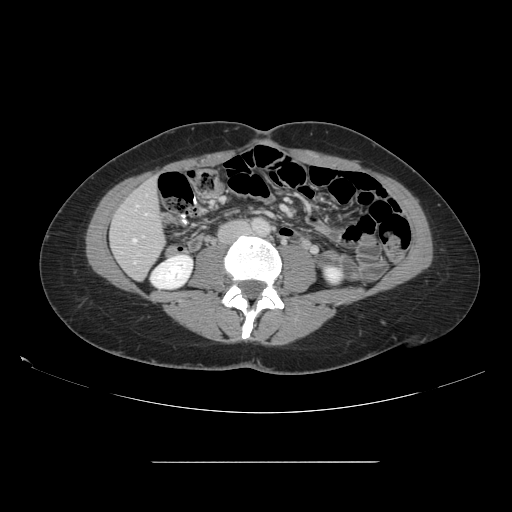
Contrast-enhanced abdominal CT, one axial slice; position 33 of 151 along the scan axis; 120 kVp; intravenous contrast given; soft-tissue window (W 400 / L 40 HU); 512 × 512 image matrix. Female patient, age 46 years. From the clinical record (not read from this slice): diagnosis: colorectal cancer liver metastases, imaged before liver resection; multiple liver metastases: yes; largest metastasis: 3 cm; chemotherapy before resection: no.
Structures marked on this image (manually delineated by an expert):
- hepatic veins: bounding box (x1, y1, x2, y2) in pixels: (133, 239, 136, 242)
- liver: (111, 180, 165, 279)
- planned liver remnant (the part of the liver to remain after resection): (111, 180, 165, 280)